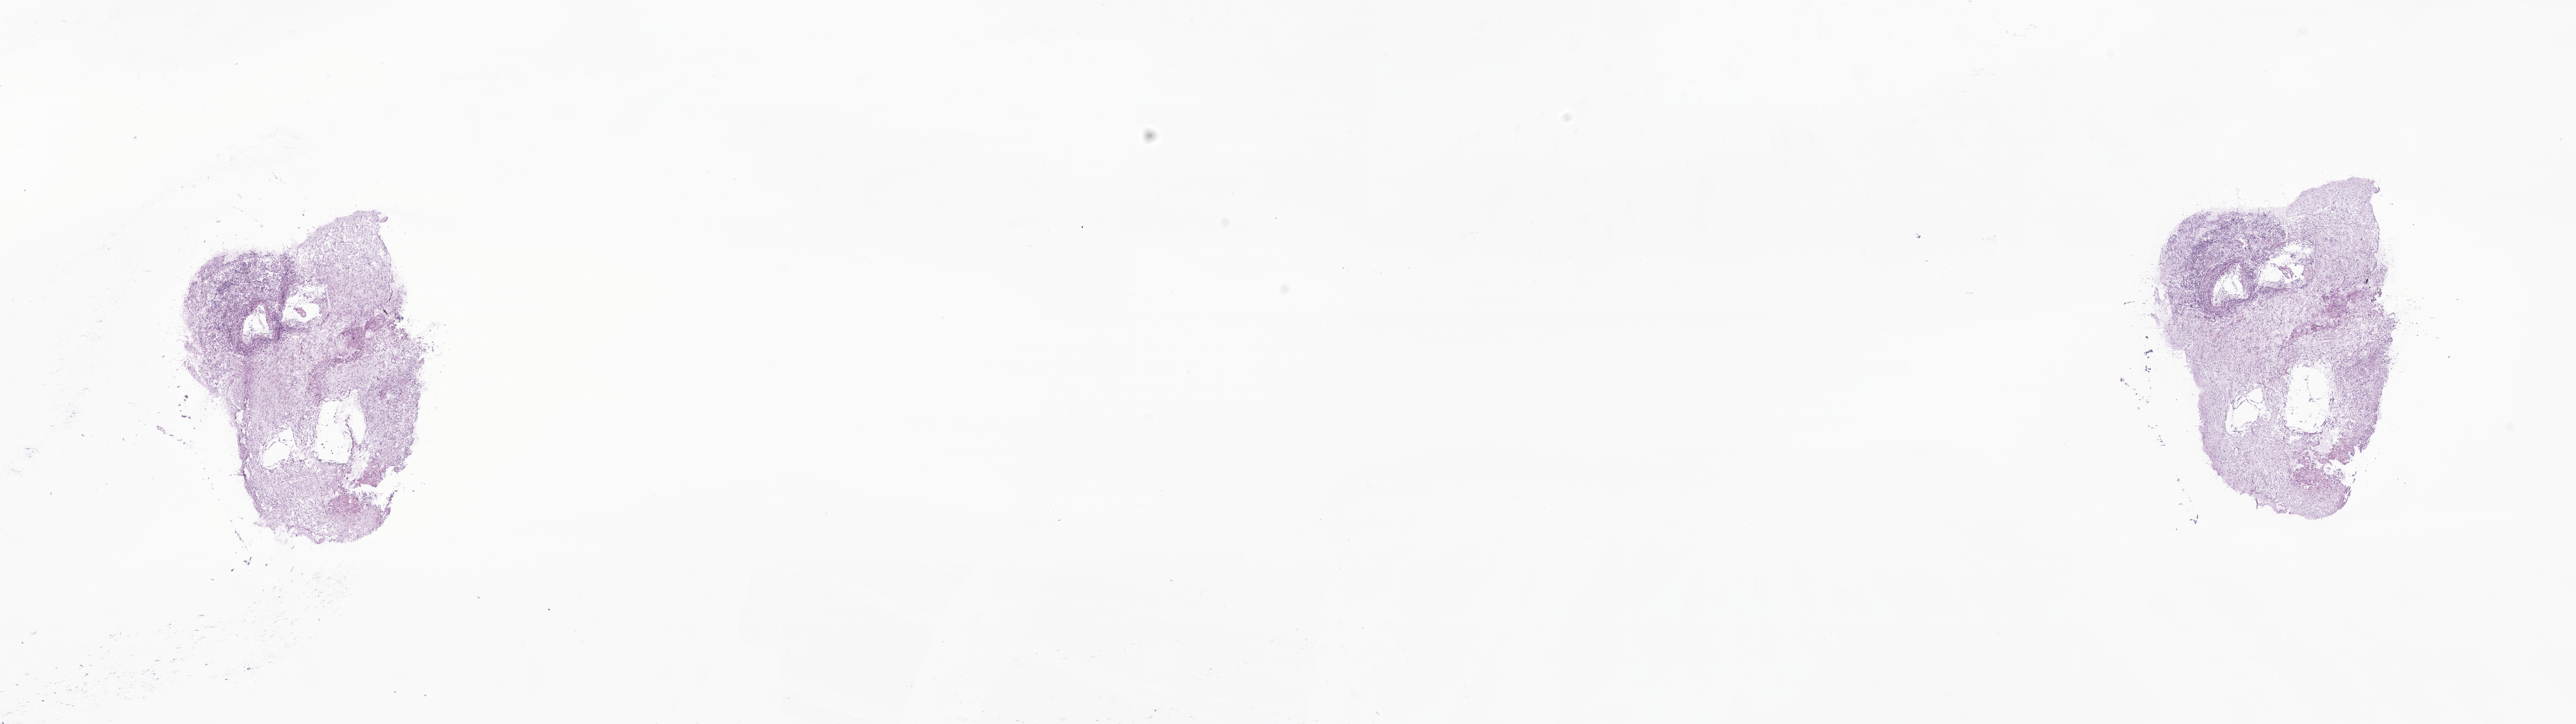
H&E whole-slide image of tumor tissue from the brain — shown as a low-resolution overview of the whole scanned area (about 26.6 x 7.5 mm), frozen section. Female patient, age 302 days.
Recorded diagnosis: Neoplasm, uncertain whether benign or malignant.